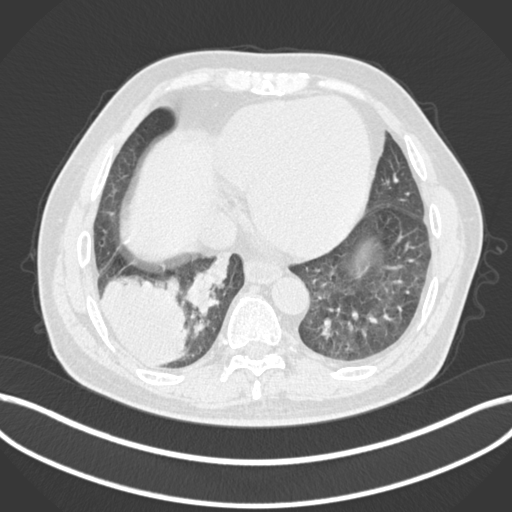
Chest CT, one axial slice. Position 40 of 200 along the scan axis. Reconstruction kernel B30f. Lung window (W 1500 / L -600 HU). 1 mm slice thickness. 512 × 512 image matrix. Male patient, age 59 years.
Annotated regions visible in this slice (bounding box drawn by a radiologist):
- lung tumour (recorded histology: adenocarcinoma): box from (x=93, y=266) to (x=192, y=367) px